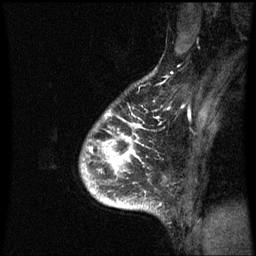
Breast MRI (dynamic contrast-enhanced), one sagittal slice. Position 53 of 60 along the scan axis. Dynamic contrast-enhanced series, image 2 of 3 at this slice position (ordered by acquisition). 1.5 T. TE 4.2 ms, TR 8.9 ms. 256 × 256 image matrix. Patient: female, 35 years. Case-level facts recorded for this patient, not image findings: setting: breast cancer imaged before/during neoadjuvant chemotherapy; receptor status: HR-positive, HER2-negative.
Structures marked on this image (semi-automatically segmented with operator editing):
- analysis volume of interest (the breast-tissue region the enhancement analysis was run in; not a lesion): bounding box (x1, y1, x2, y2) in pixels: (83, 114, 148, 209)
- tumour enhancement mask (voxels above the 70 % enhancement threshold inside the analysis volume of interest): (85, 126, 142, 209)